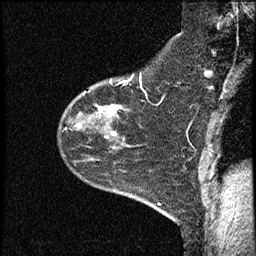
Breast MRI (dynamic contrast-enhanced), one sagittal slice. Slice 48 of 60 in the series (ordered by position). Dynamic contrast-enhanced study with each time point stored as its own series, time point 2 of 4 at this slice position (early post-contrast, ordered by acquisition time). 1.5 T. TE 4.2 ms, TR 17.6 ms. 2 mm slice thickness. 256 × 256 image matrix, field of view 200 × 200 mm. Female patient, age 53 years. From the clinical record (not read from this slice): setting: breast cancer imaged before/during neoadjuvant chemotherapy; receptor status: HR-positive, HER2-negative.
Annotated regions visible in this slice (semi-automatic segmentation, software-assisted and operator-edited):
- analysis volume of interest (the breast-tissue region the enhancement analysis was run in; not a lesion): bounding box <58,69,153,199> (left, top, right, bottom; pixels)
- tumour enhancement mask (voxels above the 100 % enhancement threshold inside the analysis volume of interest): <77,105,121,135>